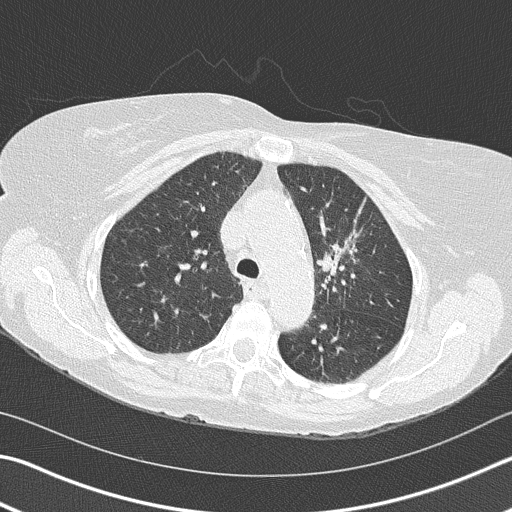
Axial slice from a low-dose chest CT screening exam, second annual screen, lung window (W 1500 / L -600 HU), 2 mm slice thickness, lung (sharp) reconstruction kernel (B50f), 120 kVp, 512 × 512 image matrix. Female participant, aged 68 years at enrolment. Former smoker at enrolment.
- Lesion marked by an expert reader, bounding box (x1, y1, x2, y2) in pixels: (293, 194, 393, 310).
- Reader record for this screening exam (exam-level; its link to the box is not recorded): non-calcified nodule or mass ≥4 mm, left upper lobe, 4 × 2 mm, spiculated (stellate) margins, soft tissue attenuation, pre-existing on the prior screen: yes; interval growth: yes.
- Official screen result: positive, other.